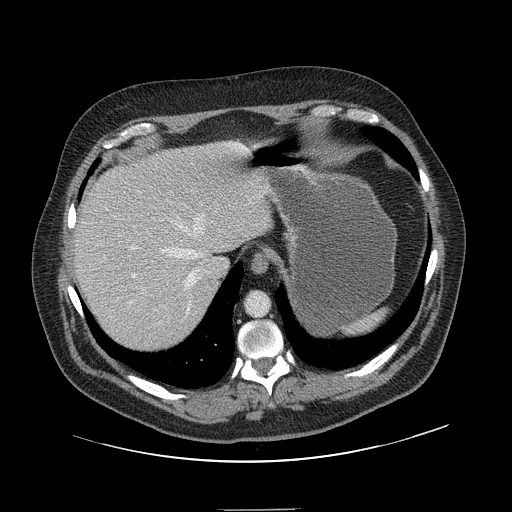
Contrast-enhanced abdominal CT, one axial slice; position 120 of 154 along the scan axis; 120 kVp; intravenous contrast given; soft-tissue window (W 400 / L 40 HU); 512 × 512 image matrix, field of view 451 × 451 mm. Male patient, age 61 years. From the clinical record (not read from this slice): diagnosis: colorectal cancer liver metastases, imaged before liver resection; multiple liver metastases: yes; largest metastasis: 2.6 cm.
Structures marked on this image (manually delineated by an expert):
- hepatic veins: bounding box (x1, y1, x2, y2) in pixels: (128, 215, 204, 324)
- liver: (74, 143, 272, 353)
- planned liver remnant (the part of the liver to remain after resection): (73, 144, 272, 350)
- portal vein (with intrahepatic branches): (115, 216, 155, 311)